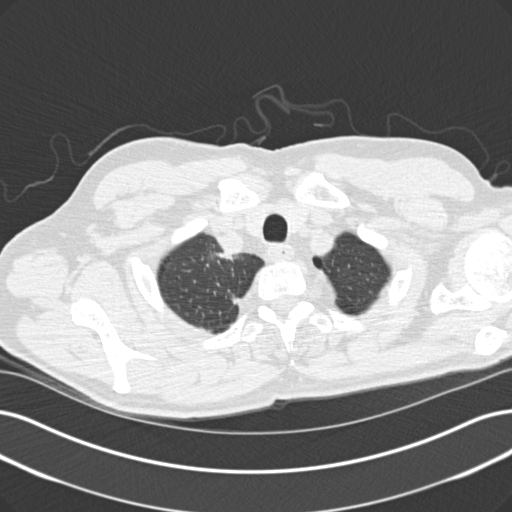
Low-dose screening chest CT, one axial slice. Position 134 of 152 along the scan axis. Reconstruction kernel B30f. 120 kVp. Lung window (W 1500 / L -600 HU). 512 × 512 image matrix.
Annotated regions visible in this slice (manually delineated by an expert):
- lesion 1 (tumor, upper lobe of right lung): bounding box <216,252,225,258> (left, top, right, bottom; pixels)